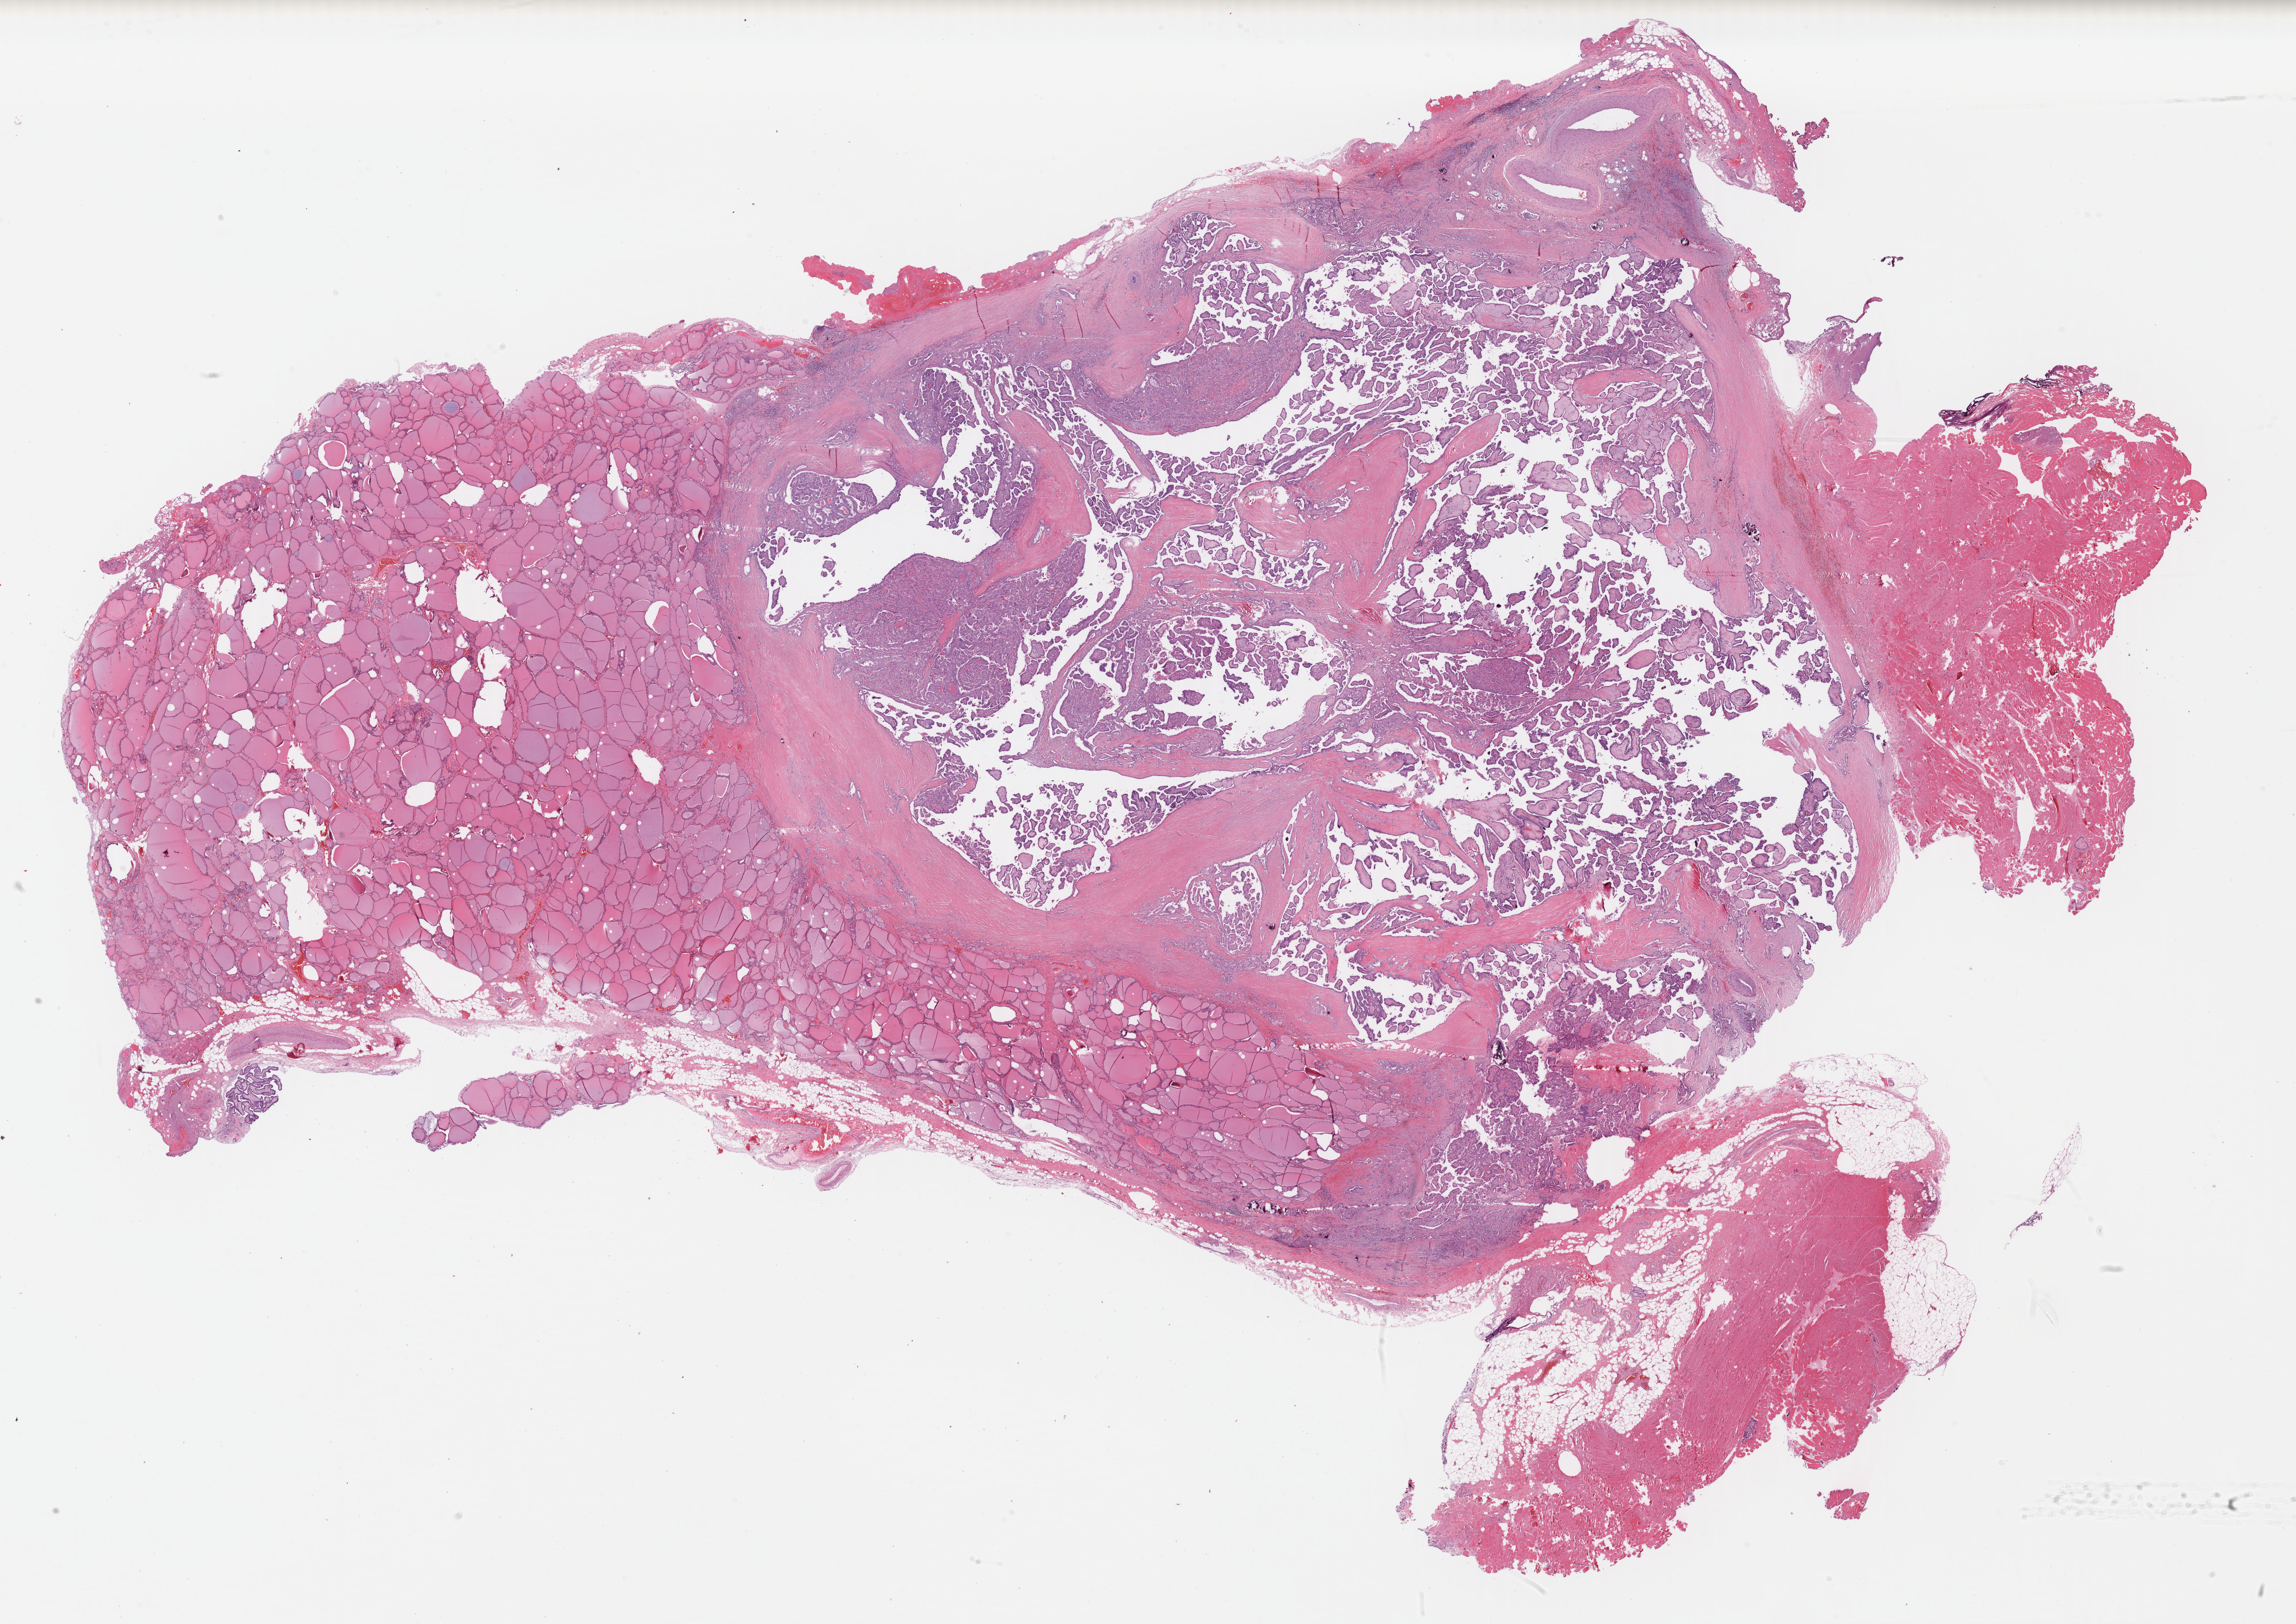
Digitized Hematoxylin and eosin (H&E) stained tissue section (whole slide) — shown as a low-resolution overview of the whole scanned area (about 31.3 x 22.2 mm), formalin-fixed paraffin-embedded (FFPE) diagnostic section, primary tumour sample from the thyroid. Patient: female, age at initial diagnosis 35 years.
* pathologic diagnosis: Papillary adenocarcinoma, NOS (thyroid gland)
* AJCC pathologic stage: I
* lymph nodes positive (case pathology): 0 of 1 examined